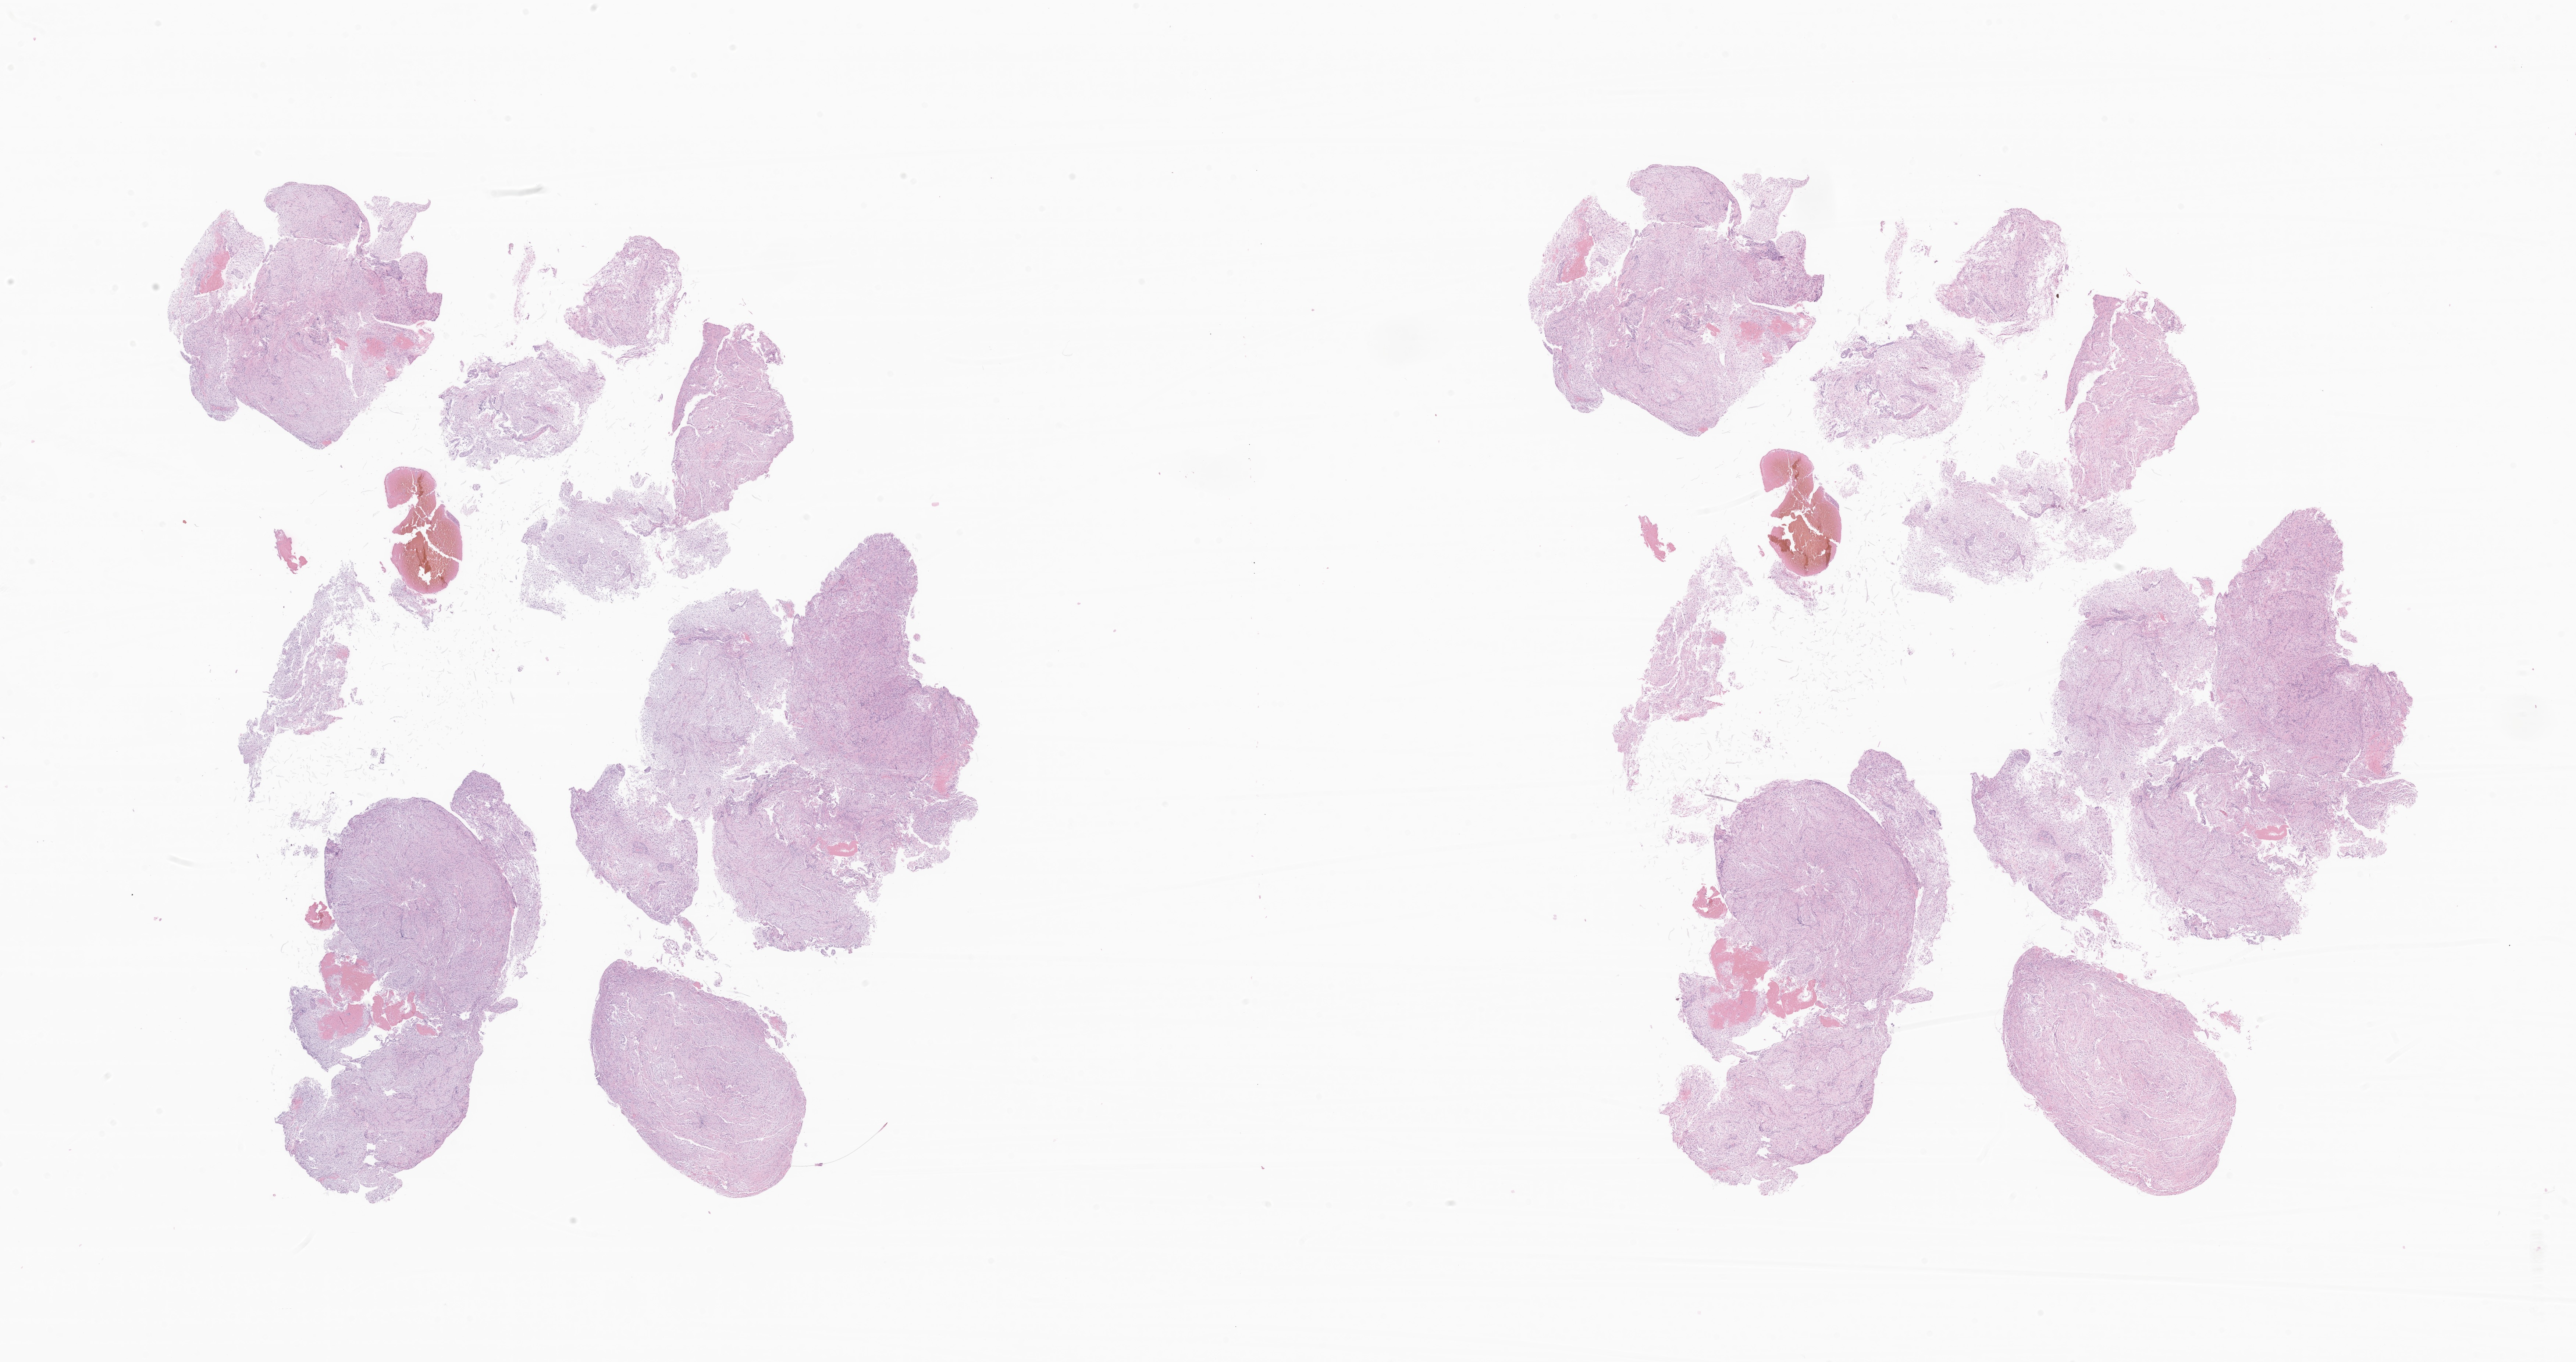
Digitized hematoxylin and eosin (H&E)-stained section of tumor tissue from the brain — shown as a low-resolution overview of the whole scanned area (about 29.5 x 15.6 mm). Patient: male, age 58 months (4 years 10 months).
Specimen: FFPE section.